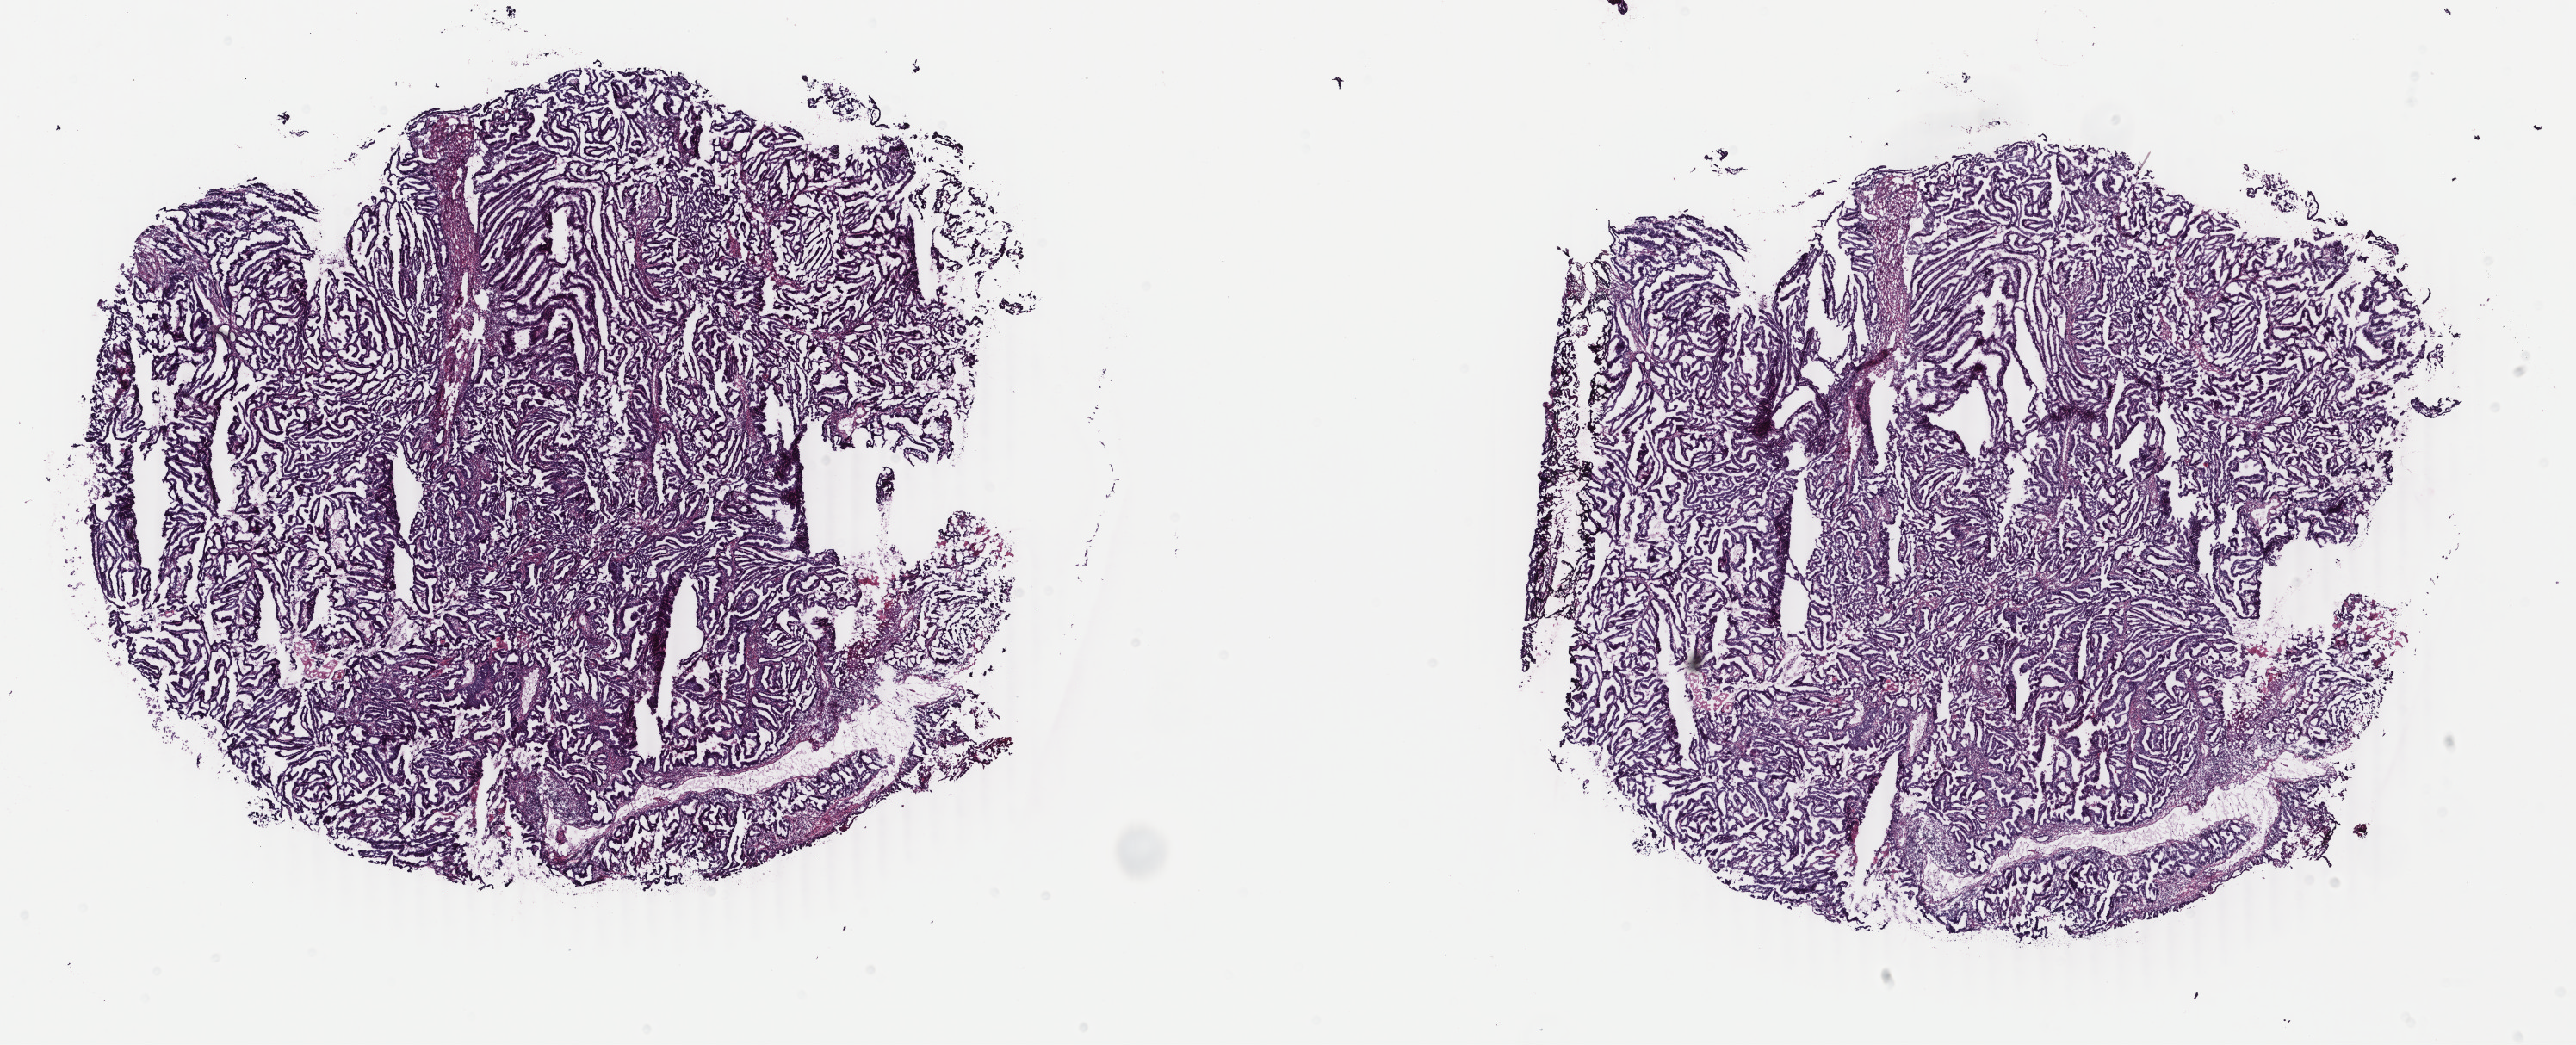
Whole-slide histology image, H&E, shown as a low-resolution overview of the whole scanned area (about 23.8 x 9.7 mm, slide scanned at 40x); frozen section from the top of the tissue portion; uterus, primary tumour sample. Female, age 55 years at initial diagnosis. Histologic grade: G1 (well differentiated). Composition of this section per pathologist review: tumour cells 80%, tumour nuclei 80%, normal cells 0%, stromal cells 15%, necrosis 5%. Inflammatory infiltration, as recorded: lymphocyte infiltration 30%, monocyte infiltration 20%, neutrophil infiltration 40%.
FIGO stage: IIIC. Histologic diagnosis: Endometrioid adenocarcinoma, NOS (endometrium). Lymph nodes positive (case pathology): 3 of 4 examined.